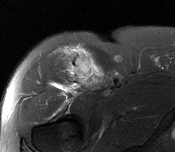
MRI of an extremity soft-tissue mass, one axial slice. Slice 112 of 116 in the series (ordered by position). T2-weighted fat-saturated. MR volume resampled by the dataset authors to the PET/CT grid (not the native acquisition matrix). 3.27 mm slice thickness. 175 × 152 image matrix, field of view 171 × 148 mm. Male patient. Case-level facts recorded for this patient, not image findings: histological type: pleiomorphic leiomyosarcoma; grade: intermediate; site of the primary tumour: right thigh.
Outlined on this slice (expert contour drawn on MRI and transferred to this co-registered scan by the dataset authors):
- gross tumour volume including surrounding oedema: bounding box [x1, y1, x2, y2] px = [69, 54, 98, 85]